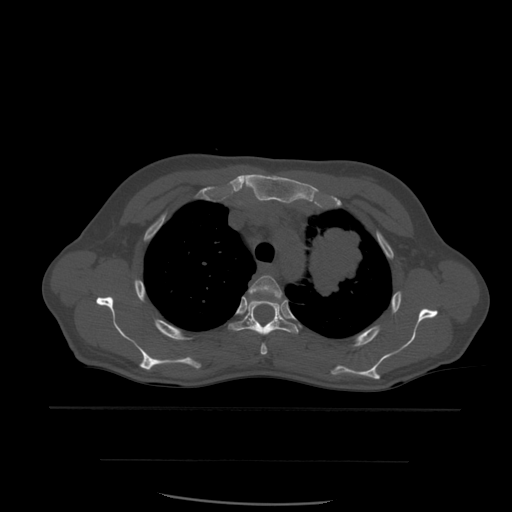
CT including the spine, one axial slice. Position 431 of 574 along the scan axis. Bone window (W 1800 / L 400 HU). 1.25 mm slice thickness. 512 × 512 image matrix, field of view 392 × 392 mm. Patient age 48 years. From the clinical record (not read from this slice): primary cancer: lung.
Outlined on this slice (semi-automatic segmentation, software-assisted and operator-edited):
- T3 vertebra: bounding box (x1, y1, x2, y2) in pixels: (249, 275, 282, 355)
- T4 vertebra: (229, 300, 299, 336)